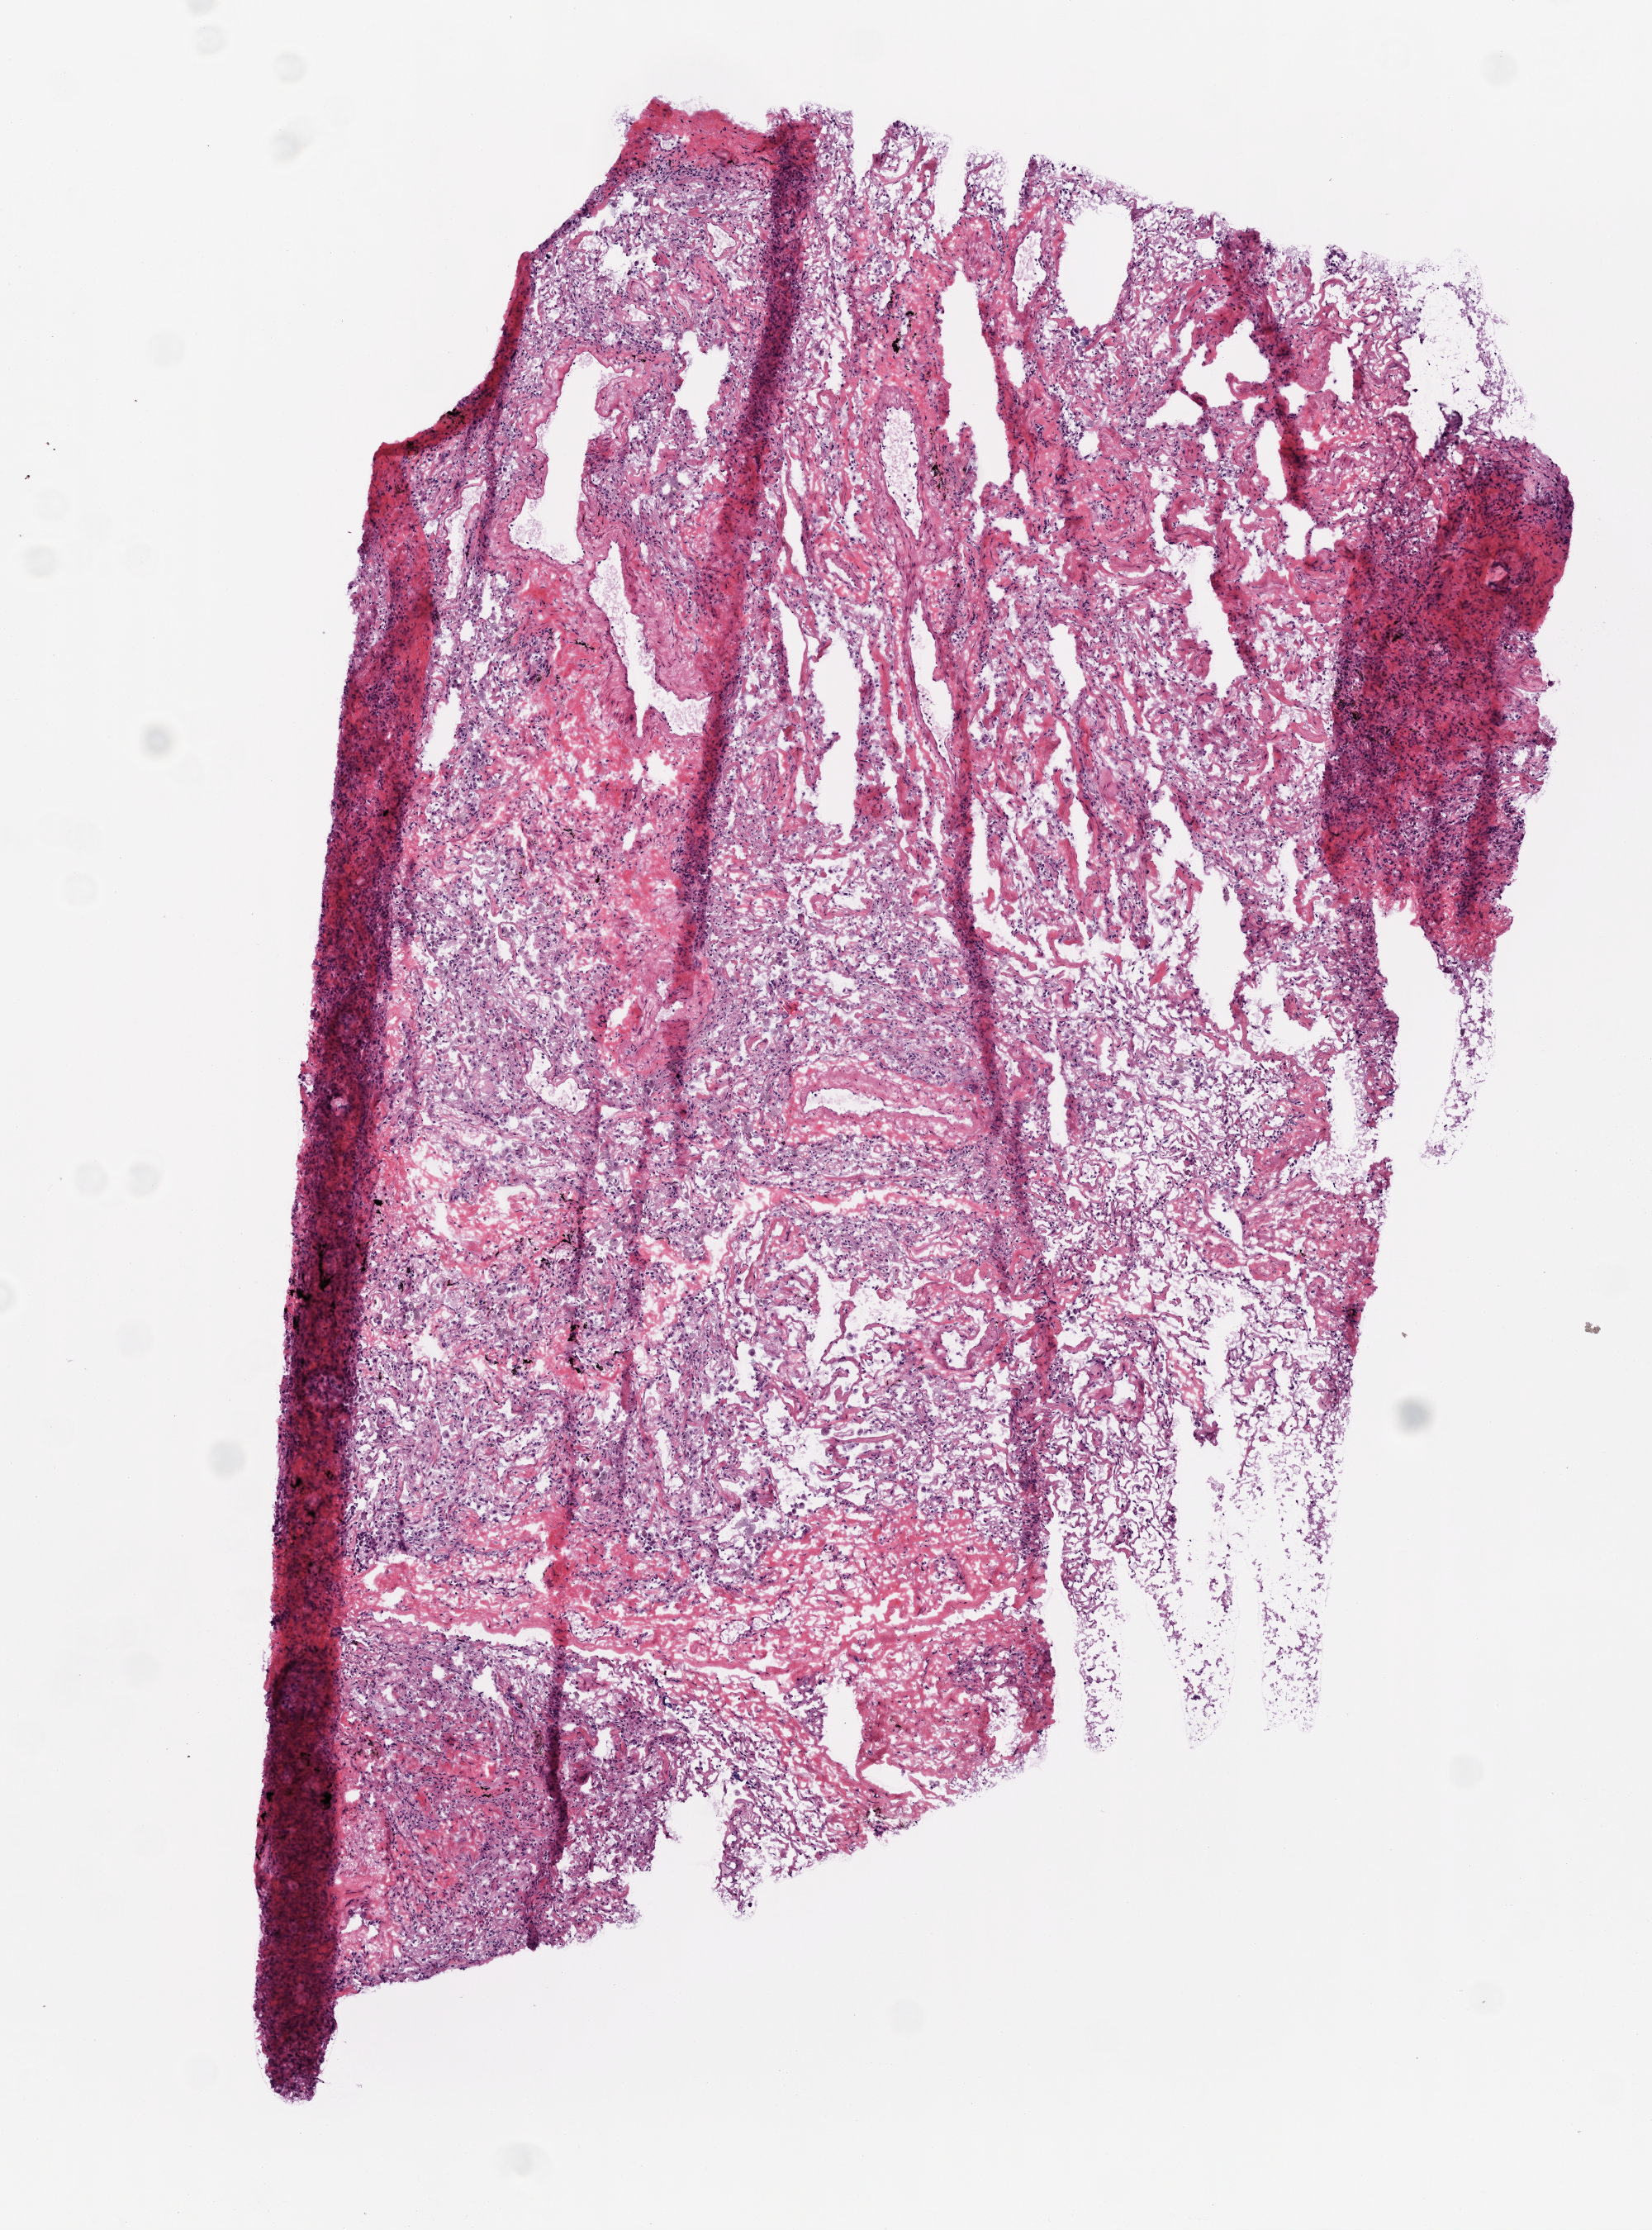
Digitized Hematoxylin and eosin (H&E) stained tissue section (whole slide), a low-resolution overview of the entire scanned area, about 4.0 x 5.4 mm (slide scanned at 20x), frozen section from the top of the tissue portion, solid tissue normal (non-tumour tissue) sample from the lung. Patient: male, age at initial diagnosis 66 years.
This section: solid tissue normal (non-tumour) sample from the same patient. Patient diagnosis: Squamous cell carcinoma, NOS (upper lobe, lung).